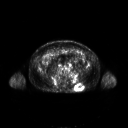
FDG PET of an extremity soft-tissue mass (from a PET/CT study), one axial slice. Position 93 of 267 along the scan axis. 3.27 mm slice thickness. 128 × 128 image matrix, field of view 700 × 700 mm. Male patient, age 61 years. From the clinical record (not read from this slice): histological type: pleiomorphic leiomyosarcoma; grade: high; site of the primary tumour: left buttock.
Structures marked on this image (expert contour drawn on MRI and transferred to this co-registered scan by the dataset authors):
- gross tumour volume including surrounding oedema: box from (x=75, y=84) to (x=83, y=91) px
- gross tumour volume (mass): (x=75, y=84)–(x=83, y=91)